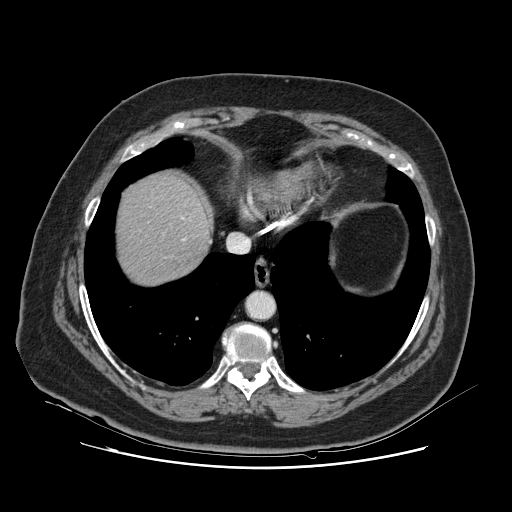
Contrast-enhanced abdominal CT, one axial slice. Position 111 of 132 along the scan axis. Intravenous contrast given. Soft-tissue window (W 400 / L 40 HU). 2.5 mm slice thickness. 512 × 512 image matrix, field of view 391 × 391 mm. Female patient, age 73 years. From the clinical record (not read from this slice): diagnosis: colorectal cancer liver metastases, imaged before liver resection.
Outlined on this slice (expert manual segmentation):
- hepatic veins: box from (x=182, y=217) to (x=185, y=241) px
- liver: (x=118, y=175)–(x=209, y=284)
- planned liver remnant (the part of the liver to remain after resection): (x=118, y=175)–(x=208, y=284)